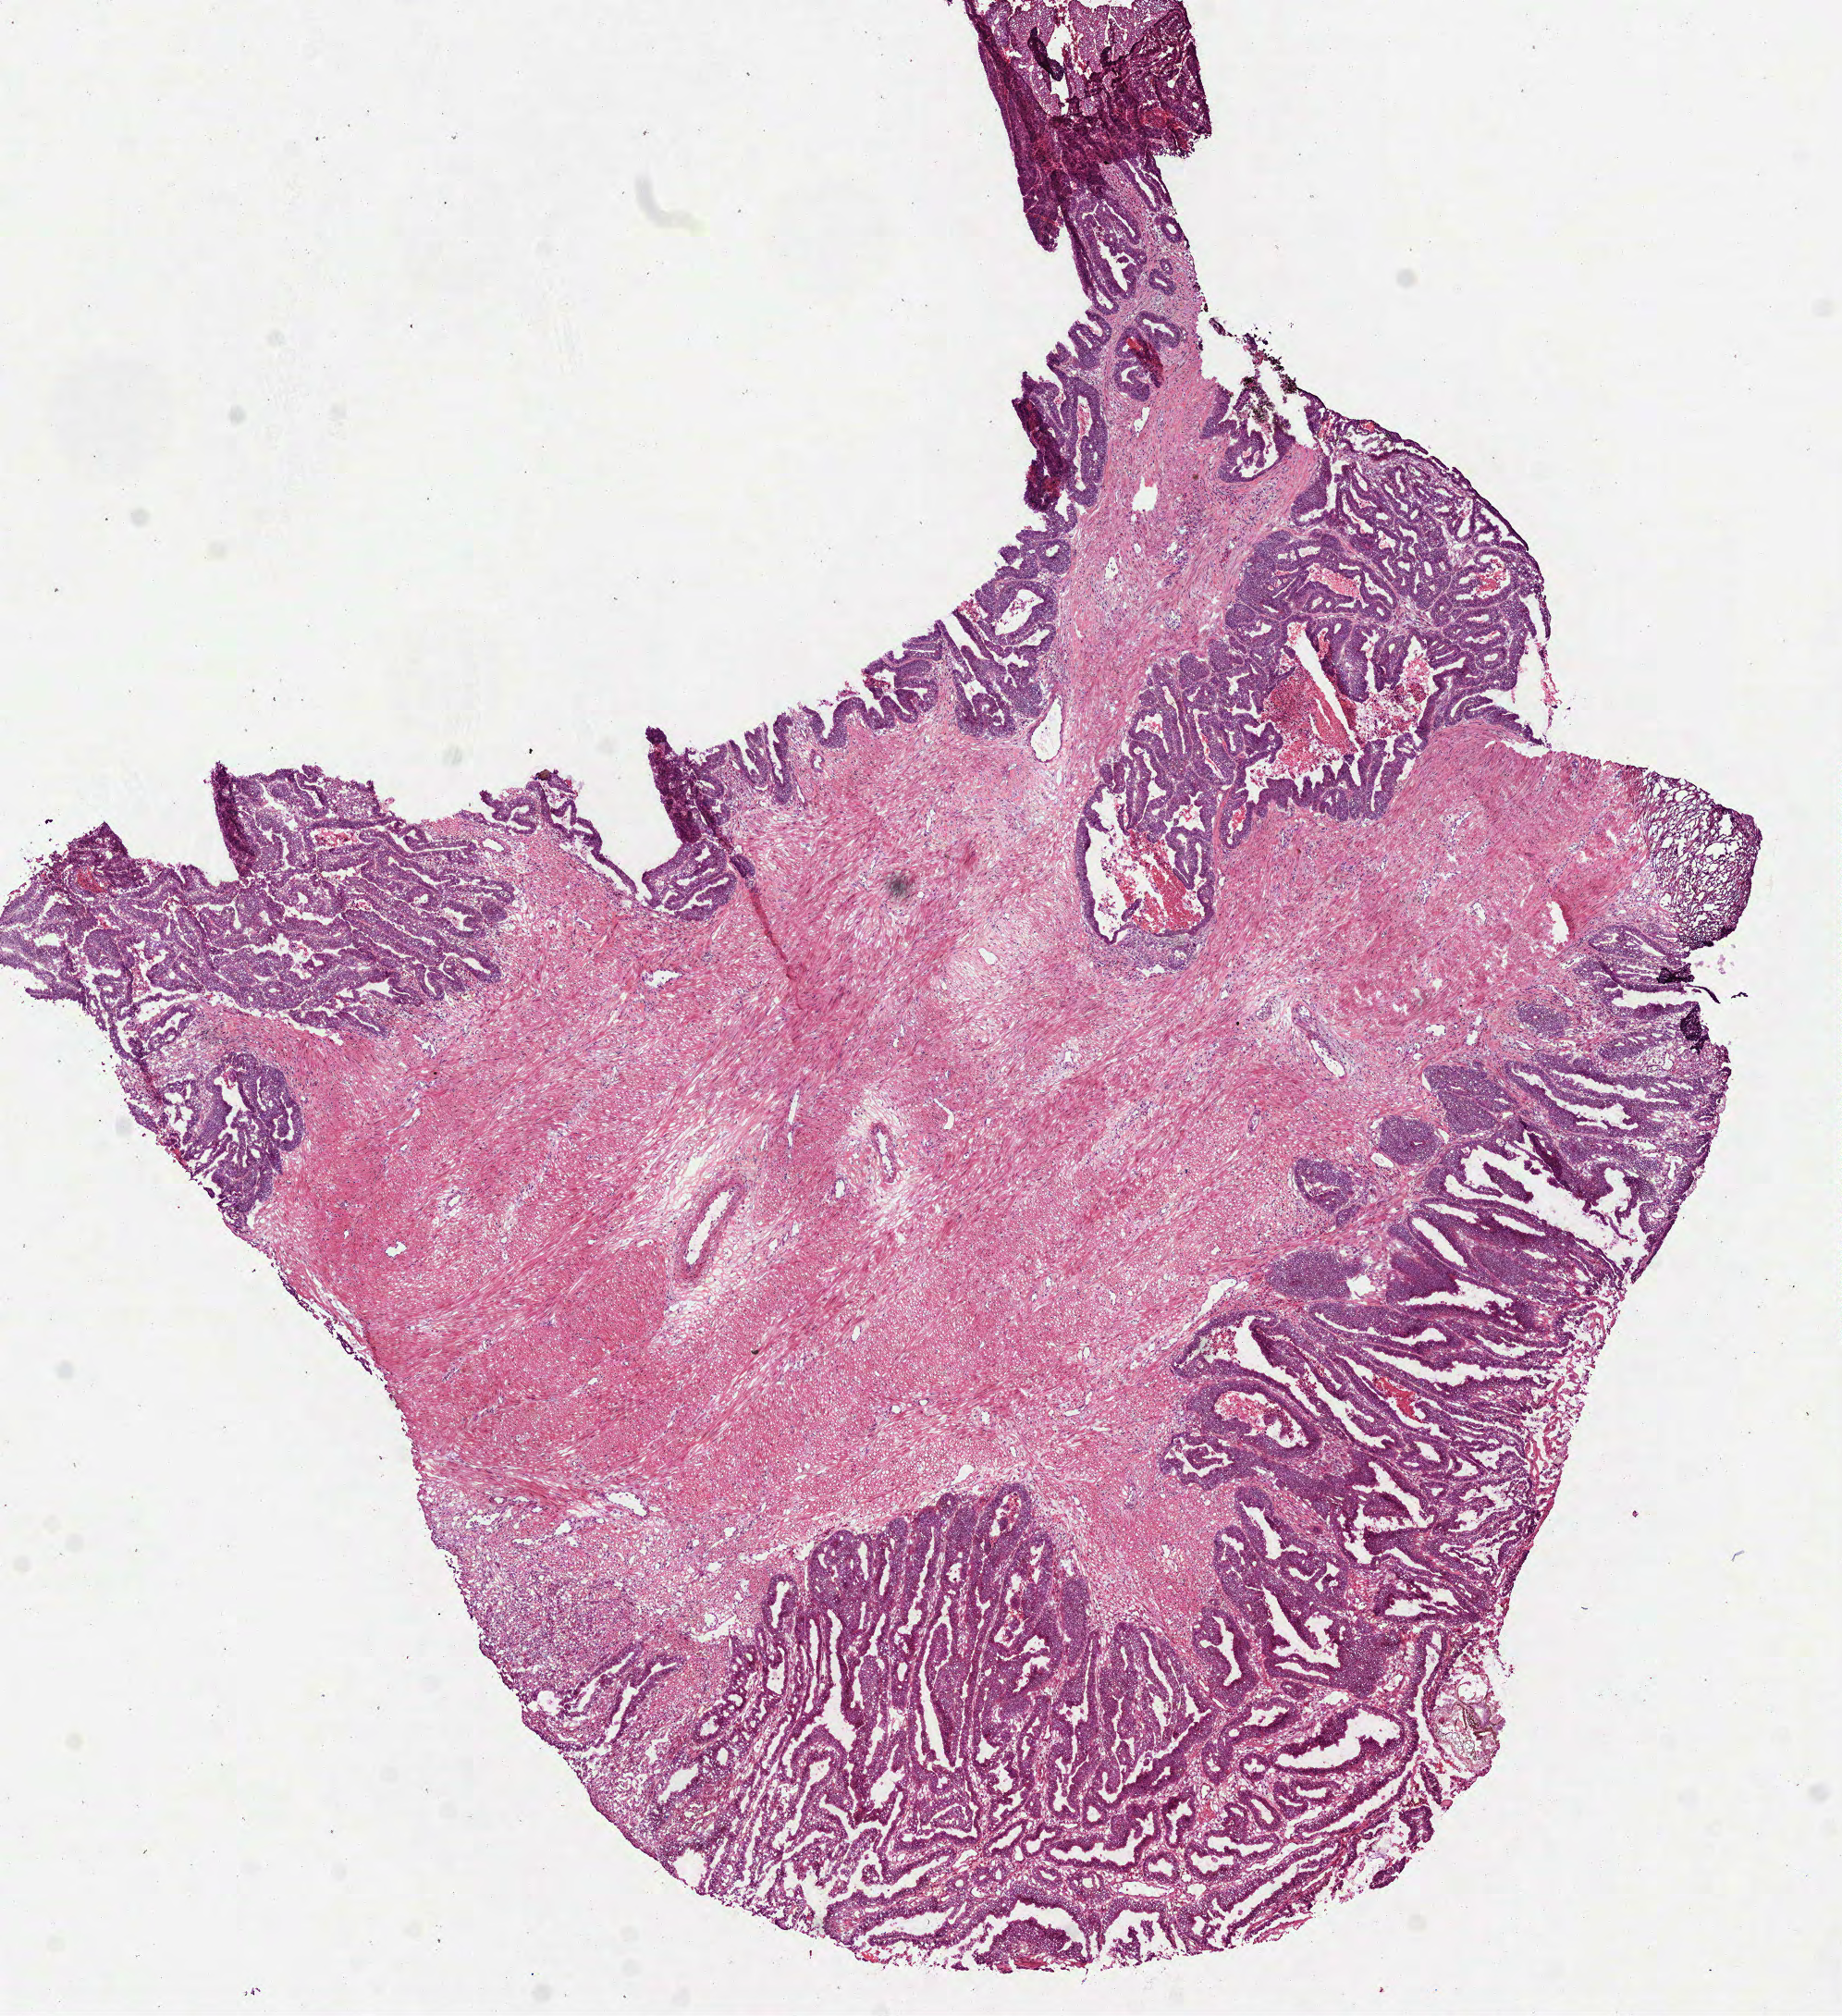
Whole-slide histology image, H&E — whole scanned area (about 8.0 x 8.8 mm) shown as a low-resolution overview. Frozen section from the top of the tissue portion. Colon, primary tumour sample. Patient: male, age at initial diagnosis 59 years. Composition of this section per pathologist review: tumour cells 50%, tumour nuclei 80%, normal cells 40%, stromal cells 0%, necrosis 10%. Inflammatory infiltration, as recorded: lymphocyte infiltration 5%, monocyte infiltration 2%, neutrophil infiltration 5%.
AJCC pathologic stage: IVA. Histologic diagnosis: Adenocarcinoma, NOS (sigmoid colon). TNM: T3 N0 M1.